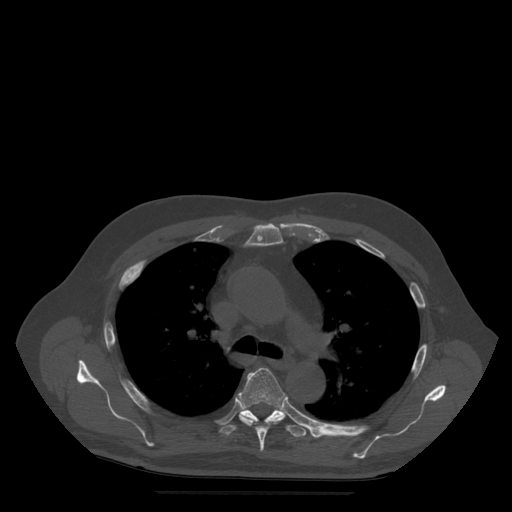
CT including the spine, one axial slice. Position 366 of 522 along the scan axis. Bone window (W 1800 / L 400 HU). 1.25 mm slice thickness. 512 × 512 image matrix. Patient age 72 years. Case-level facts recorded for this patient, not image findings: primary cancer: prostate.
Outlined on this slice (semi-automatically segmented with operator editing):
- T5 vertebra: bounding box [x1, y1, x2, y2] px = [238, 368, 286, 452]
- T6 vertebra: [219, 409, 307, 438]